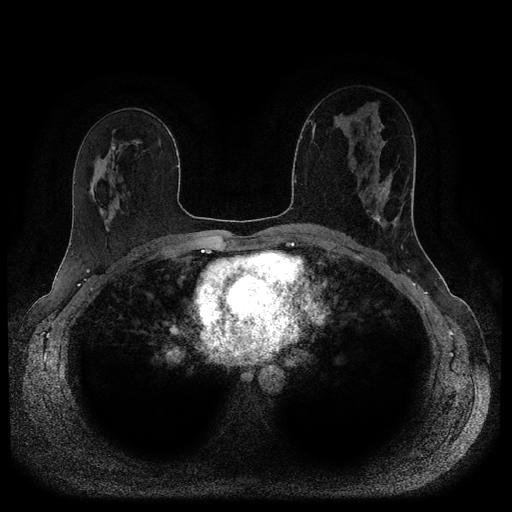
Breast MRI (dynamic contrast-enhanced, multi-phase), one axial slice; slice 56 of 116 in the series (ordered by position); dynamic contrast-enhanced series, time point 2 of 5 at this slice position (early post-contrast); 1.5 T; TE 2.6 ms, TR 5.3 ms; 512 × 512 image matrix, field of view 350 × 350 mm. Female patient, age 45 years.
Structures marked on this image (semi-automatic segmentation, software-assisted and operator-edited):
- breast lesion (labelled 'tumour' in the annotation; benign lesions carry a separate 'benign' label): box from (x=368, y=174) to (x=399, y=230) px